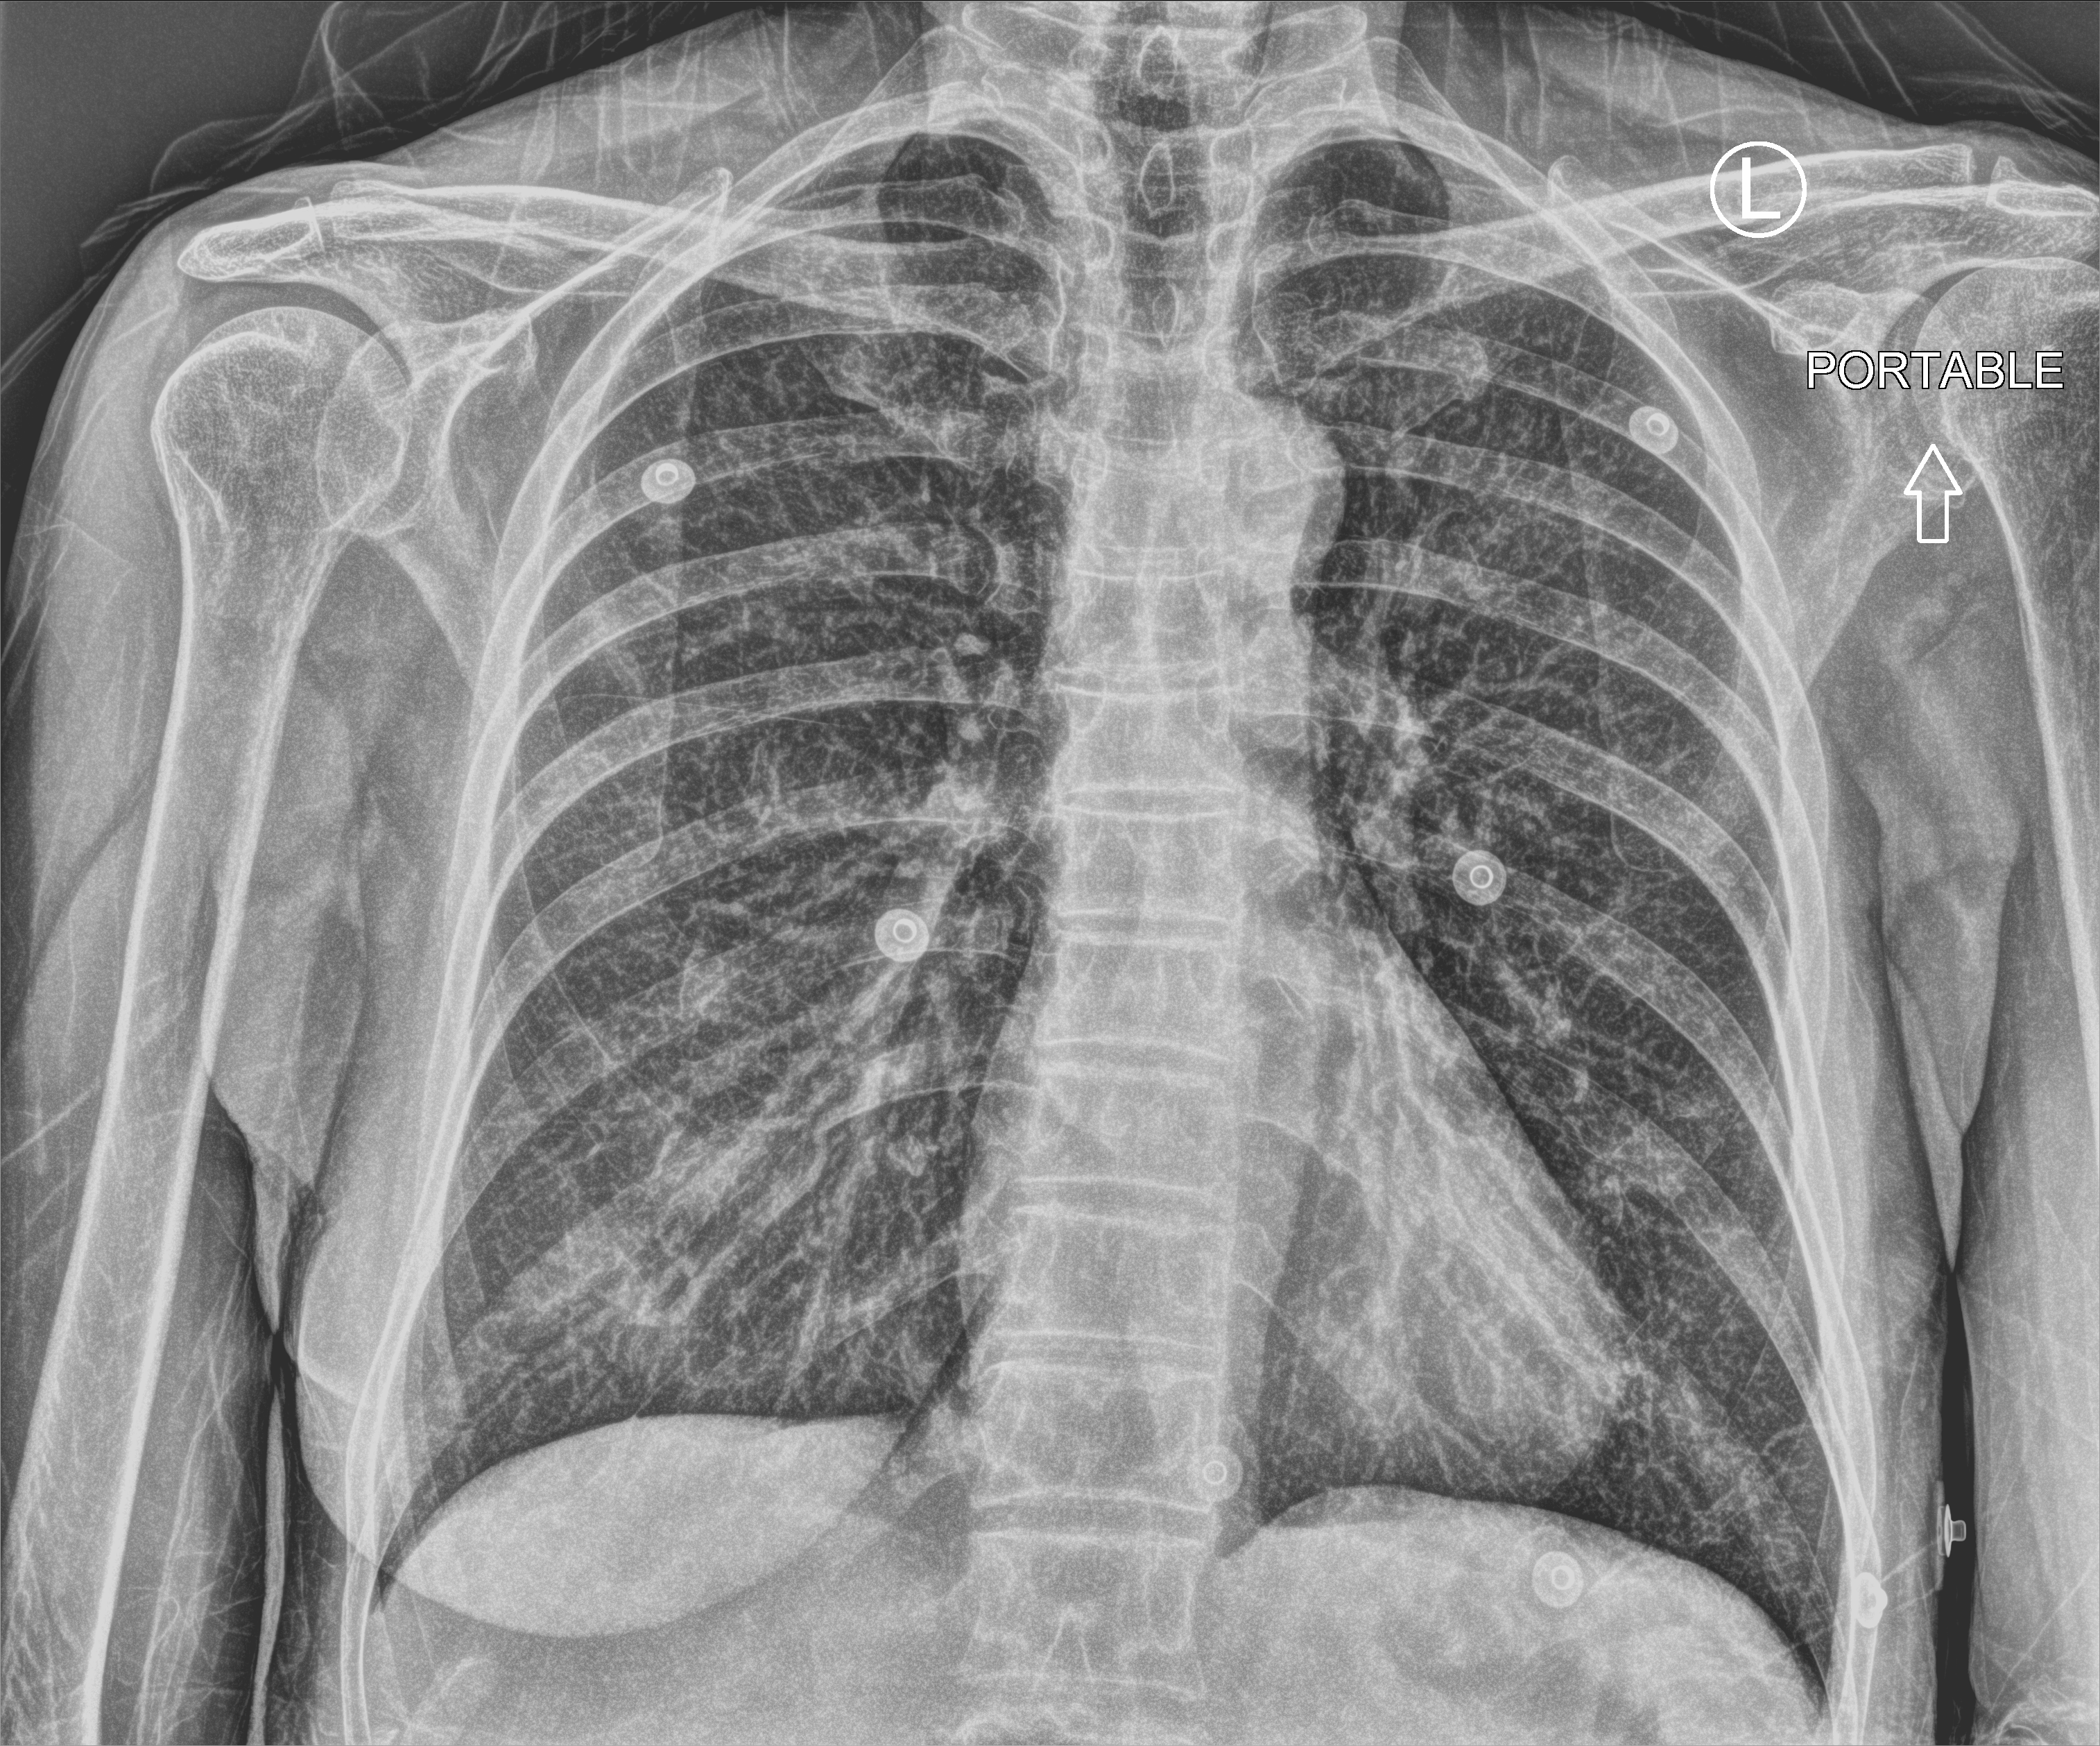
Chest X-ray (portable), anteroposterior (AP) projection. Patient hospitalised with COVID-19; female, aged 60–74 years.
Admission-level facts for this patient (not findings on this image; timing relative to this image not recorded): mechanically ventilated during this hospital stay: no; admitted to intensive care during this hospital stay: no.